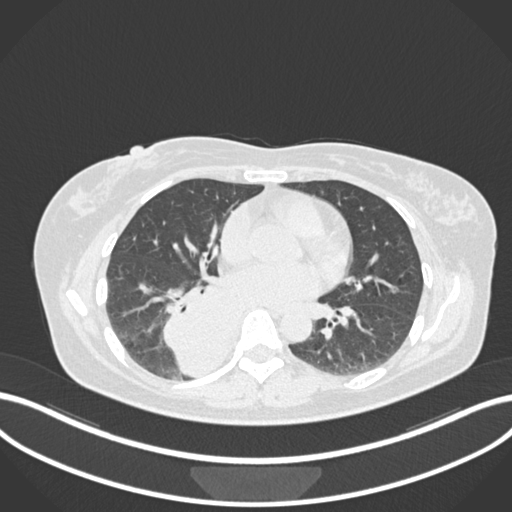
Chest CT, one axial slice; slice 578 of 677 in the series (ordered by position); reconstruction kernel B30f; lung window (W 1500 / L -600 HU); 512 × 512 image matrix, field of view 400 × 400 mm. Patient: female, 54 years. Case-level facts recorded for this patient, not image findings: clinical TNM (as recorded): T4 N0 M0.
Annotated regions visible in this slice (rectangle marked by the reading radiologist):
- lung tumour (recorded histology: adenocarcinoma): bounding box <158,279,250,376> (left, top, right, bottom; pixels)